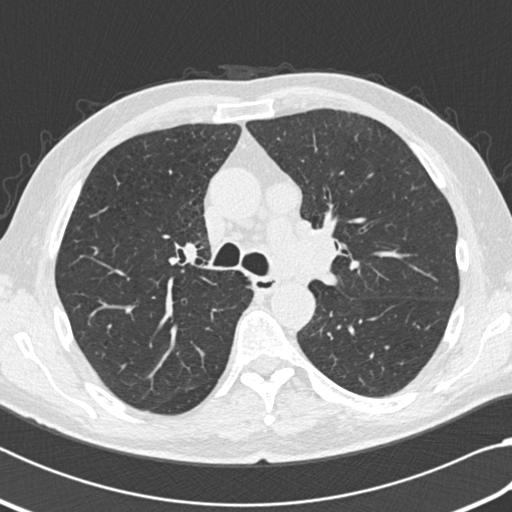
Axial slice from a low-dose chest CT screening exam. Third screening round (two years after baseline). Lung window (W 1500 / L -600 HU). 2 mm slice thickness. Standard (soft-tissue) reconstruction kernel (B30f). 120 kVp. 512 × 512 image matrix. Male, age 64 years at enrolment. Current smoker at enrolment.
• Lesion marked by an expert reader, bounding box [x1, y1, x2, y2] px = [253, 175, 301, 219].
• Screening reader's record for this exam: no non-calcified nodule ≥4 mm recorded.
• Official screen result: negative screen, significant abnormalities not suspicious for lung cancer.
• Later outcome: lung cancer diagnosed 163 days after this screen — small cell carcinoma, NOS, mediastinum, stage IV (AJCC 6th edition).